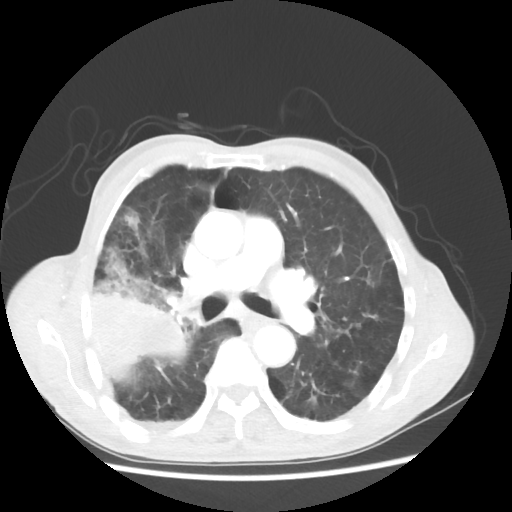
Chest CT, one axial slice. Slice 32 of 58 in the series (ordered by position). 100 kVp. Lung window (W 1500 / L -600 HU). 5 mm slice thickness. 512 × 512 image matrix. Patient: male, 75 years. Case-level facts recorded for this patient, not image findings: clinical TNM (as recorded): T4 N1 M1.
Outlined on this slice (bounding box drawn by a radiologist):
- lung tumour (recorded histology: adenocarcinoma): bounding box <81,242,198,386> (left, top, right, bottom; pixels)